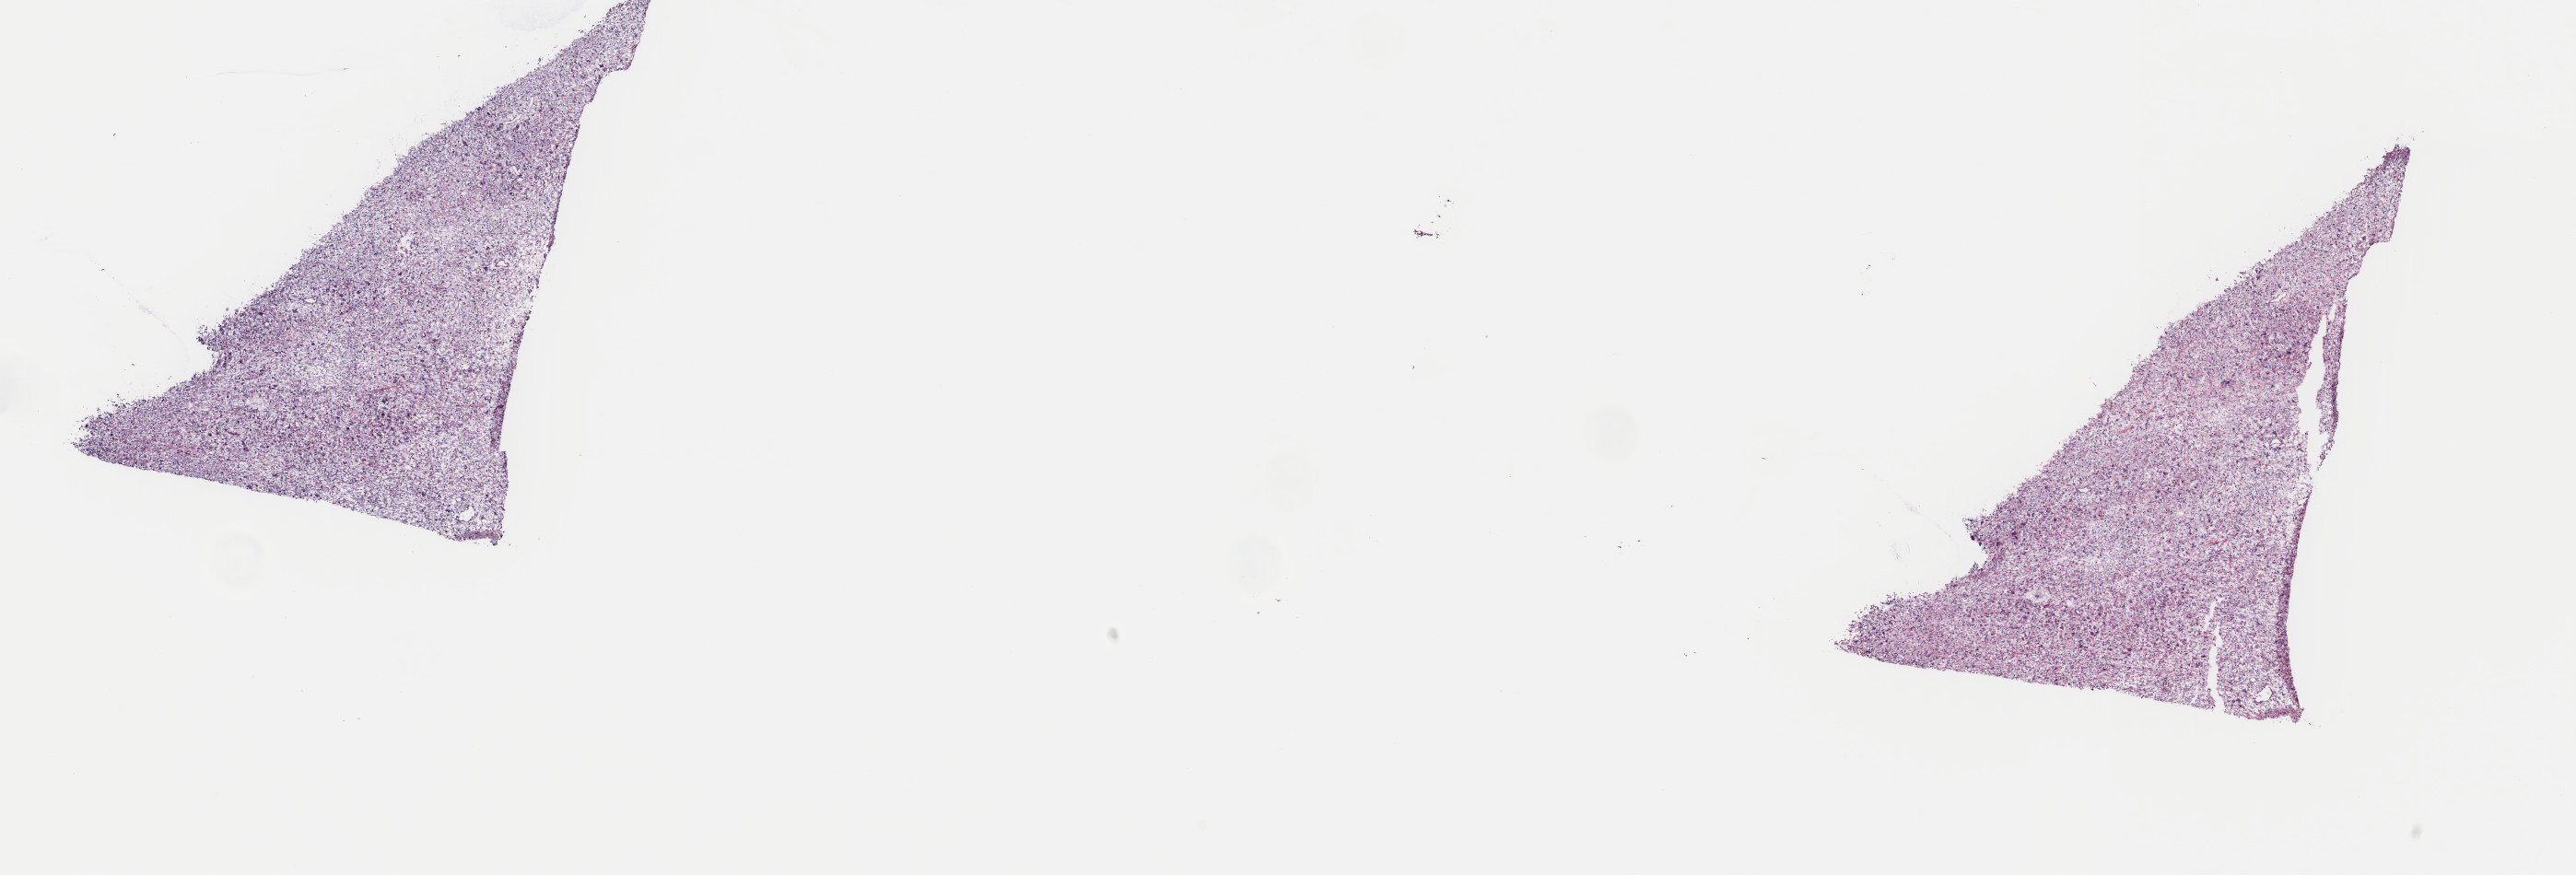
Hematoxylin and eosin (H&E) stained whole-slide image — low-resolution overview of the scanned area, about 22.2 x 7.5 mm. Frozen section from the top of the tissue portion. Primary tumour sample from the connective, subcutaneous and other soft tissues. Patient: female, age at initial diagnosis 75 years. Composition of this section per pathologist review: tumour cells 90%, tumour nuclei 95%, normal cells 0%, stromal cells 10%, necrosis 0%. Inflammatory infiltration, as recorded: lymphocyte infiltration 0%, monocyte infiltration 0%, neutrophil infiltration 0%.
Pathologic diagnosis: Malignant fibrous histiocytoma (connective, subcutaneous and other soft tissues of lower limb and hip).